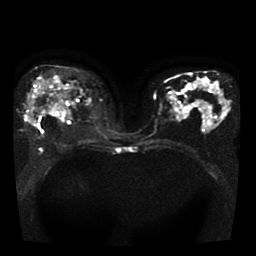
Breast MRI, one axial slice. Position 22 of 41 along the scan axis. Diffusion-weighted series; image 2 of 4 stored at this slice position (different b-values; order by instance number). 1.5 T. 256 × 256 image matrix, field of view 330 × 330 mm. Female patient.
Annotated regions visible in this slice (outlined manually by an expert reader):
- tumour on diffusion-weighted imaging: box from (x=28, y=95) to (x=38, y=123) px